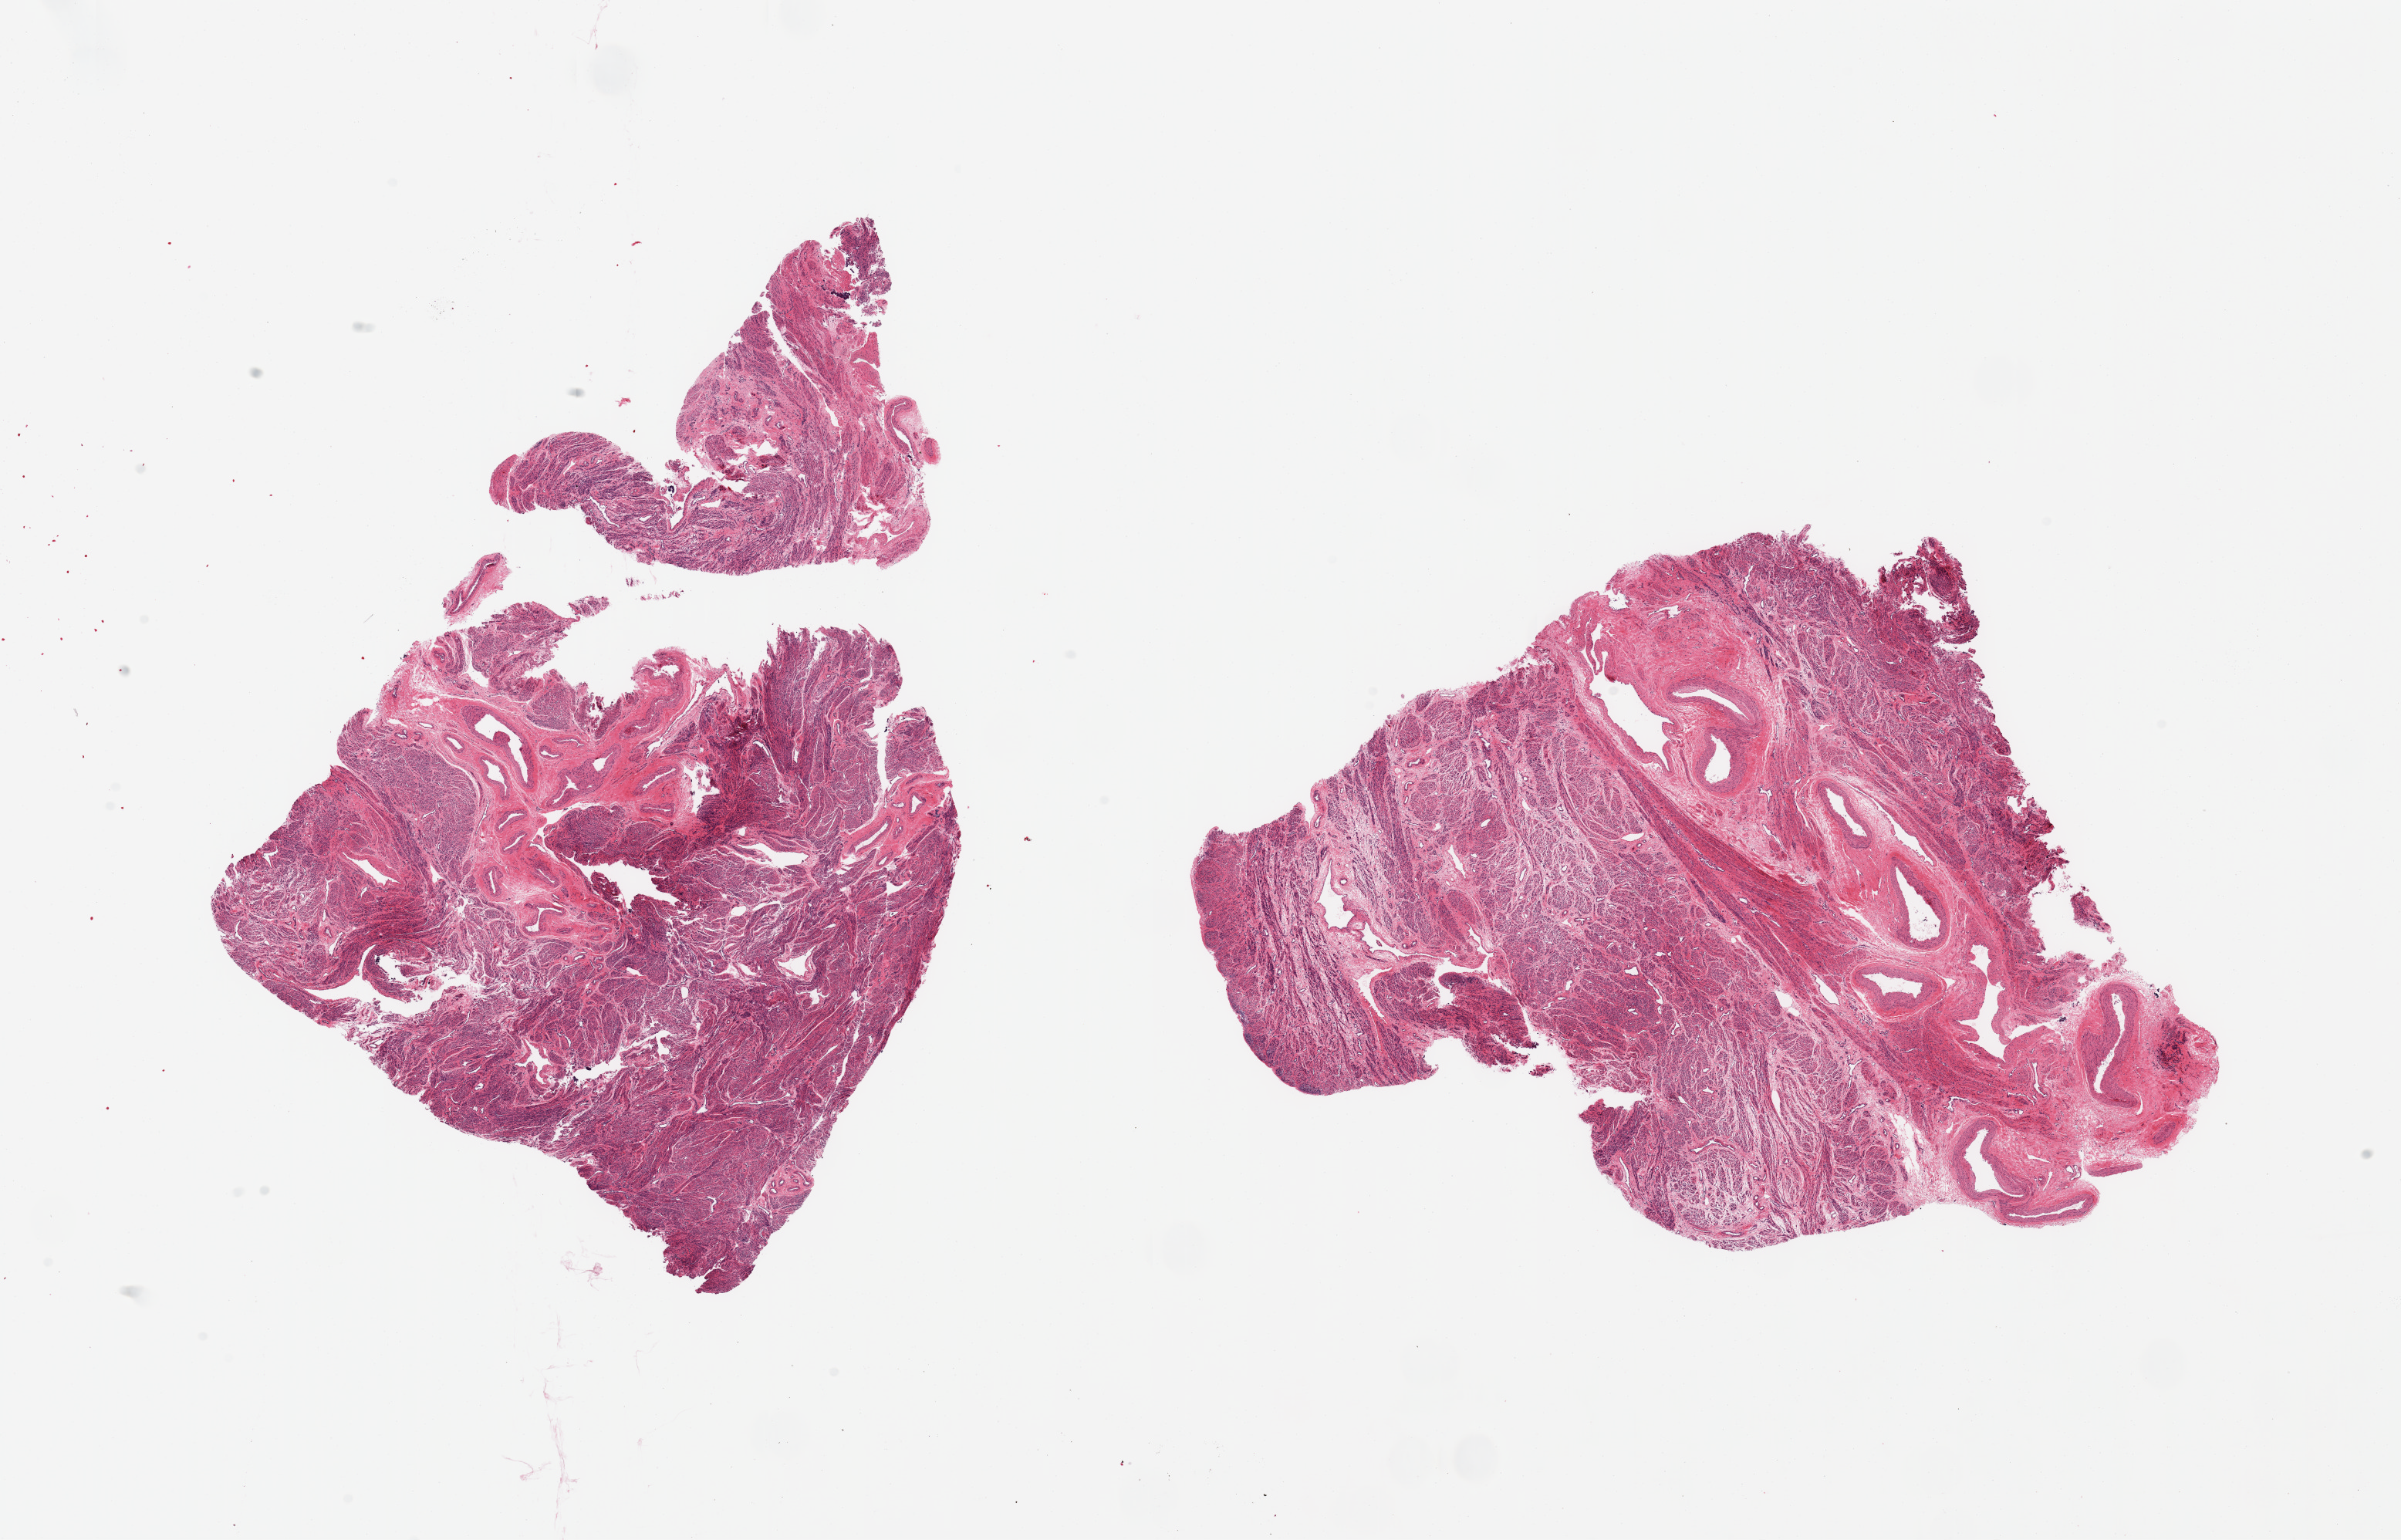
Digitized haematoxylin and eosin-stained section, brightfield — low-resolution overview of the scanned area, about 24.6 x 15.8 mm (slide scanned at 20x). PAXgene-fixed paraffin-embedded (PFPE) section. Section of uterus (target tissue). Tissue donor sample. Donor sex: female.
Reviewer comment on this tissue sample: 2 pieces; myometrium.